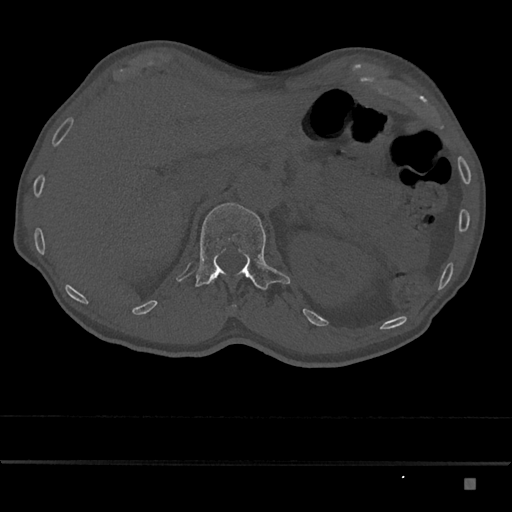
CT including the spine, one axial slice; position 557 of 797 along the scan axis; 120 kVp; bone window (W 1800 / L 400 HU); 0.5 mm slice thickness; 512 × 512 image matrix, field of view 390 × 390 mm. Male patient, age 72 years. Case-level facts recorded for this patient, not image findings: primary cancer: prostate.
Outlined on this slice (semi-automatic segmentation, software-assisted and operator-edited):
- L1 vertebra: bounding box [x1, y1, x2, y2] px = [196, 203, 290, 290]
- T12 vertebra: [210, 278, 216, 283]